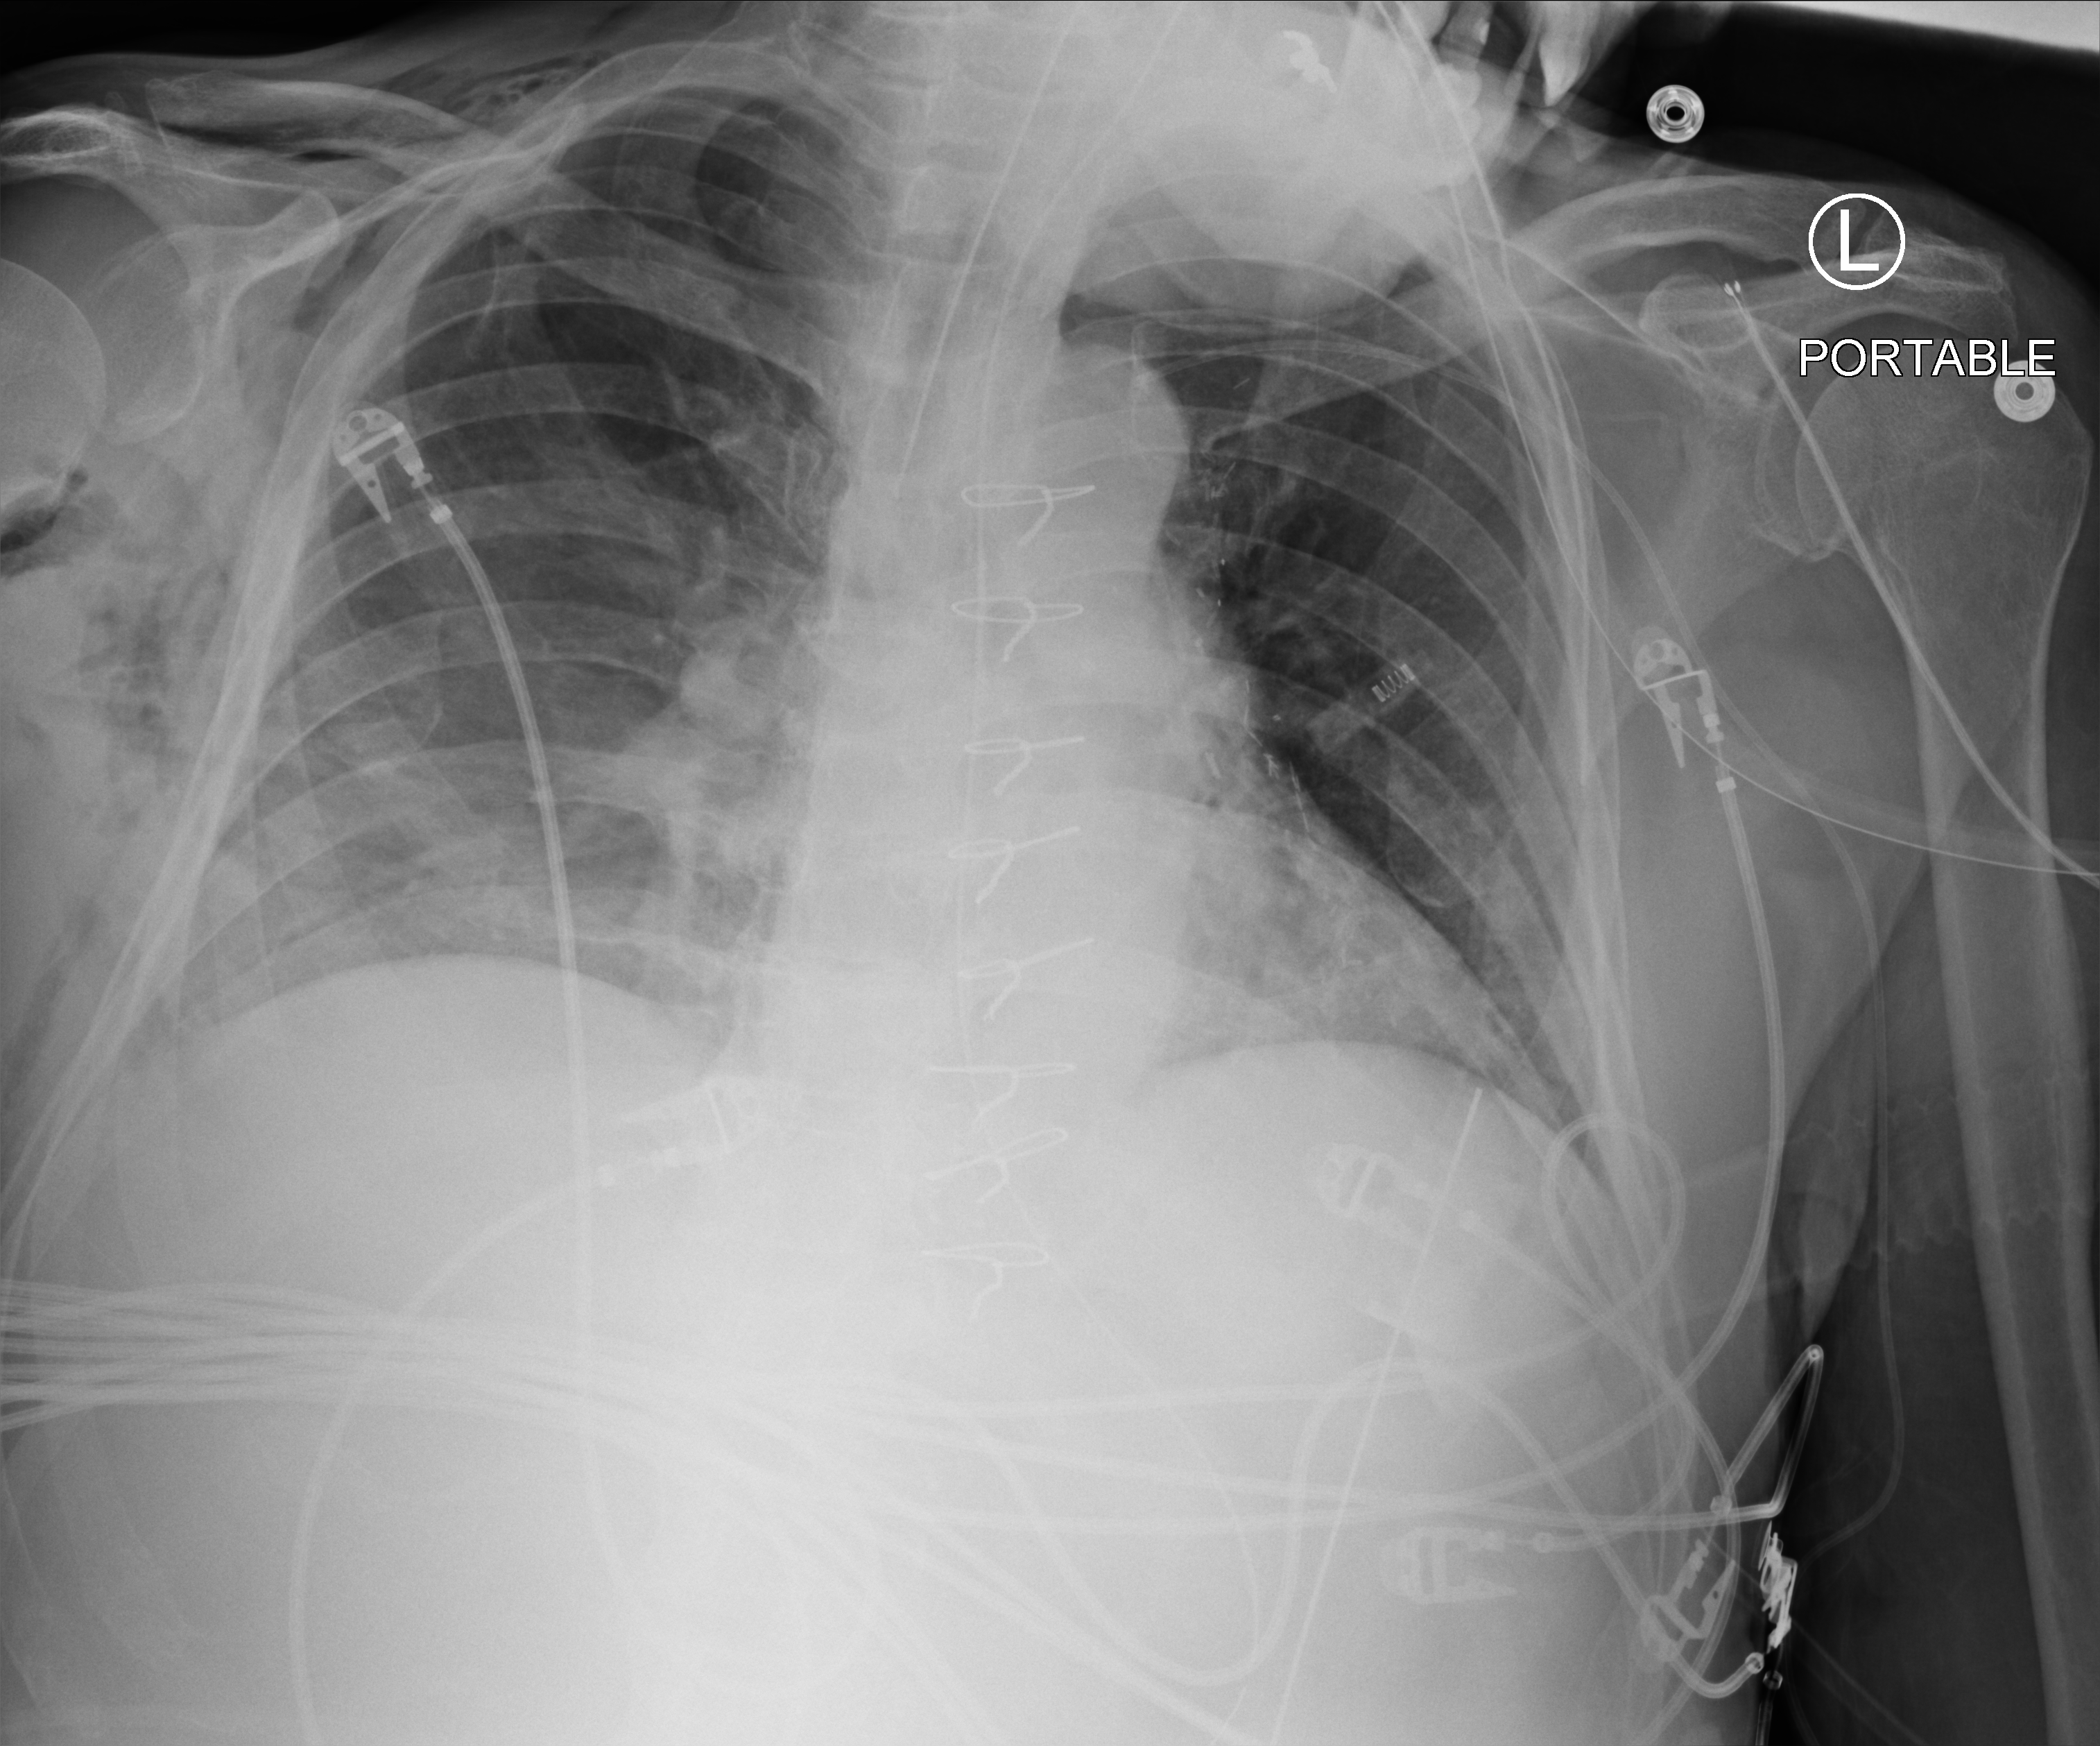
Bedside chest radiograph (computed radiography); anteroposterior (AP) projection. Patient hospitalised with COVID-19; male, aged 60–74 years.
From the hospital-stay record, not from the radiograph (when in the stay this image was taken is not recorded):
- chronic kidney disease (admission record): no